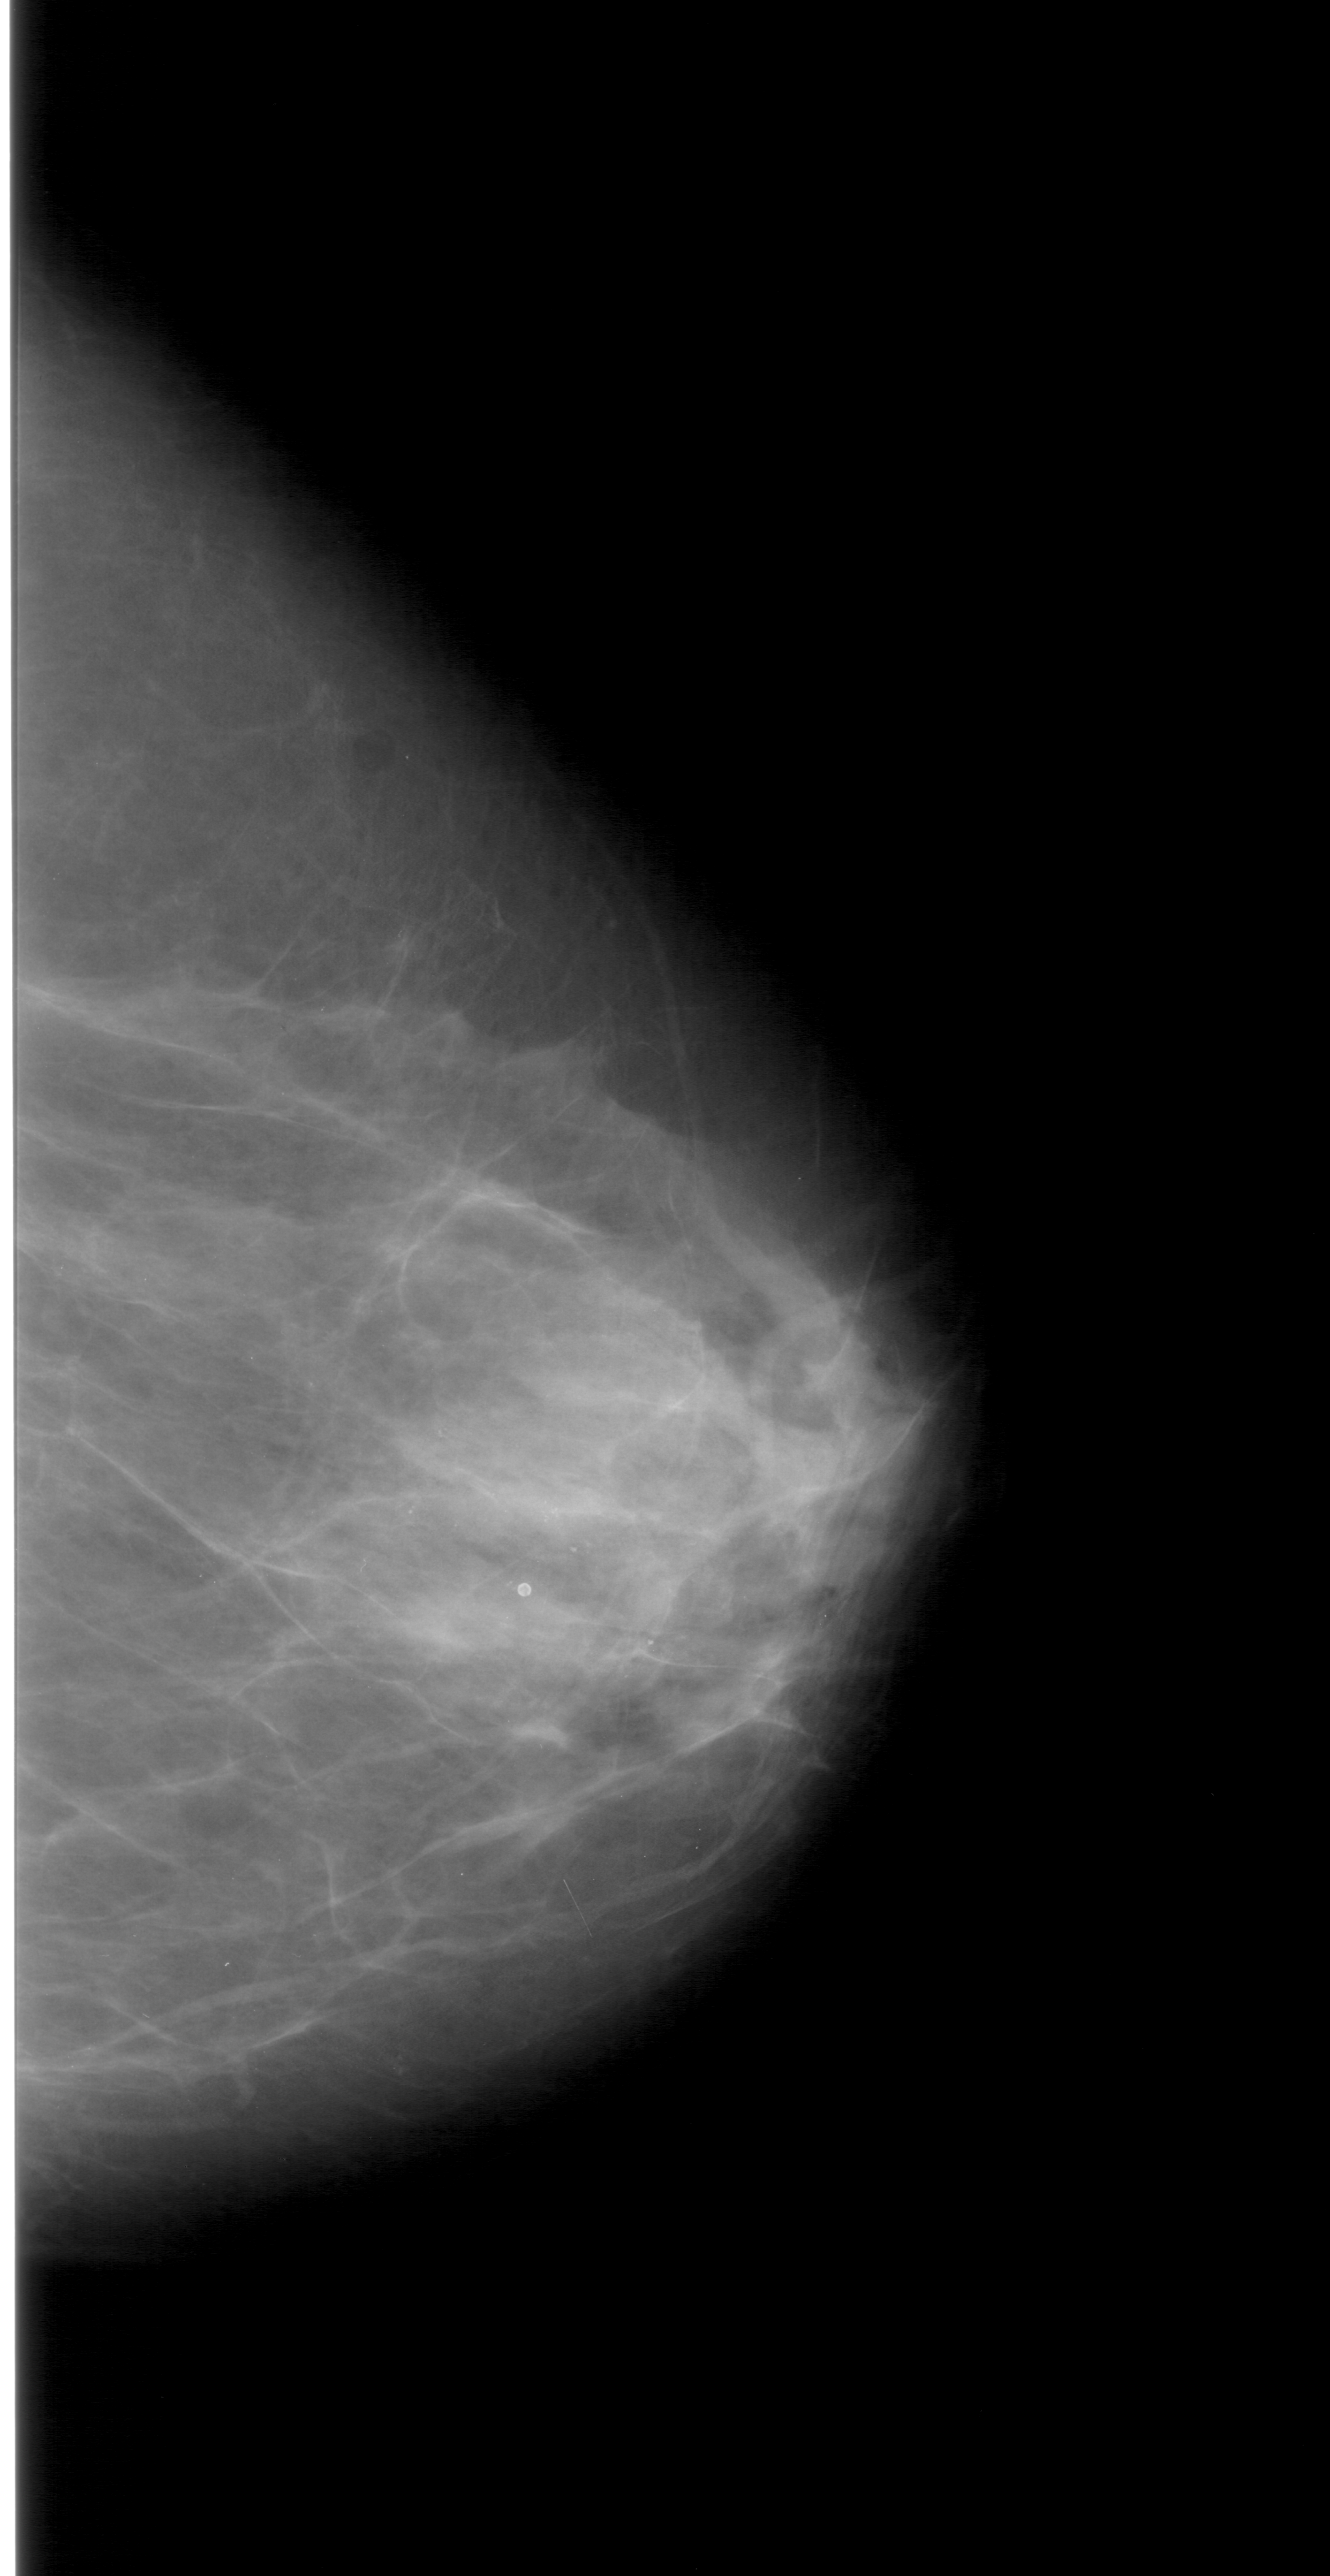
Scanned film-screen mammogram; right breast; craniocaudal (CC) view.
- Finding: calcifications, morphology pleomorphic, distribution linear; BI-RADS assessment category 4; pathology (as recorded): benign.